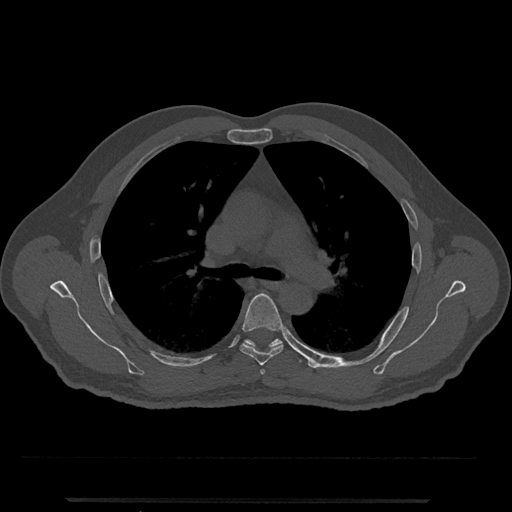
CT including the spine, one axial slice; position 779 of 797 along the scan axis; reconstruction kernel Br40s/3; bone window (W 1800 / L 400 HU); 0.5 mm slice thickness; 512 × 512 image matrix, field of view 419 × 419 mm. Patient: male, 63 years. From the clinical record (not read from this slice): primary cancer: prostate.
Outlined on this slice (semi-automatically segmented with operator editing):
- T5 vertebra: box from (x=239, y=293) to (x=283, y=366) px
- T6 vertebra: (x=244, y=338)–(x=302, y=363)